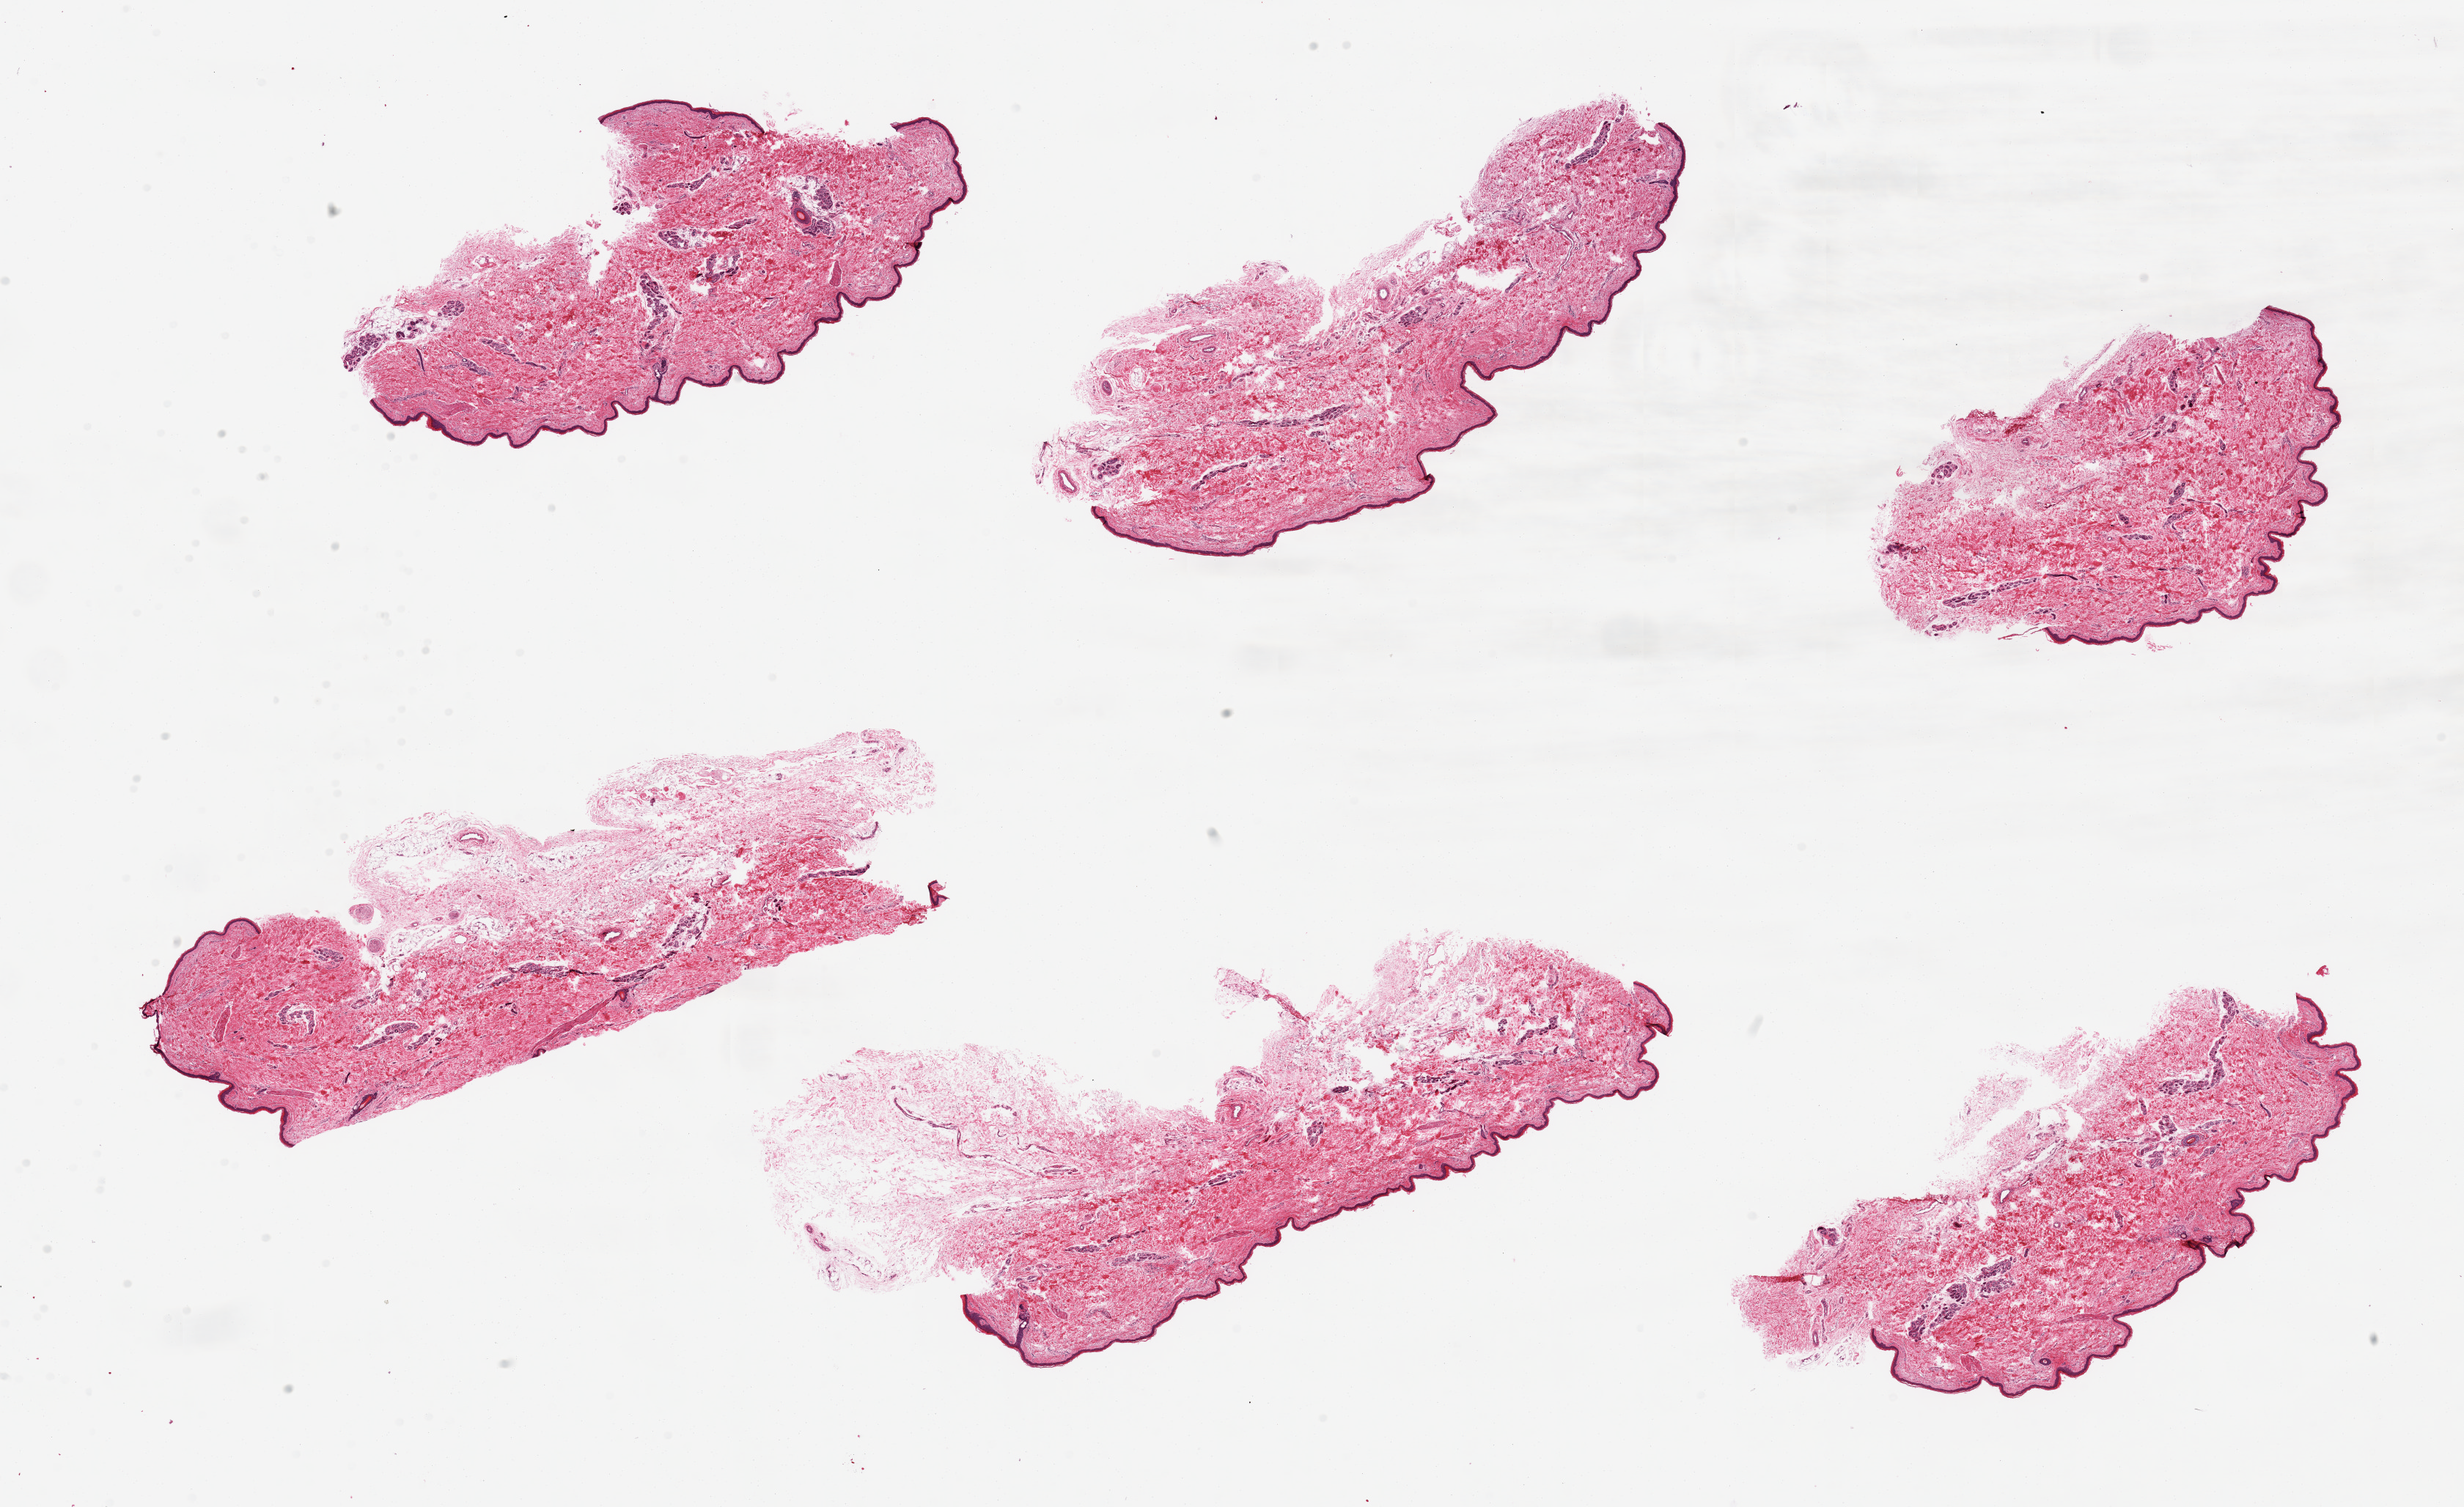
Whole-slide image, hematoxylin and eosin (H&E) stain, a low-resolution overview of the entire scanned area, about 26.6 x 16.3 mm (acquisition: 20x scan); PAXgene-fixed paraffin-embedded (PFPE) section; section of skin of lower leg (target tissue); tissue donor sample. Donor sex: female.
* pathologist's review note for this sample: 6 pieces, adherent dermal fat up to ~2mm; squamous epithelium is ~20-30 microns